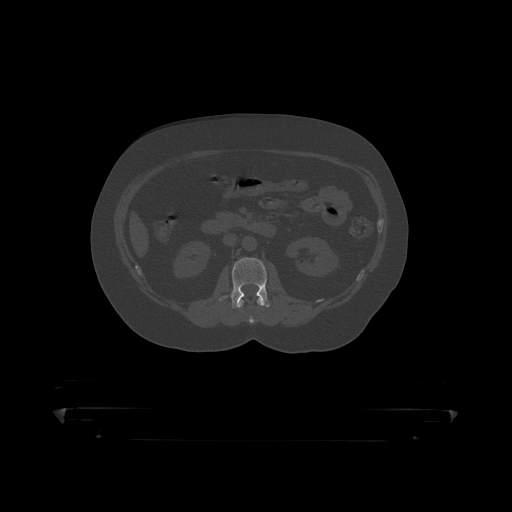
CT including the spine, one axial slice. Position 125 of 390 along the scan axis. 120 kVp. Bone window (W 1800 / L 400 HU). 1.25 mm slice thickness. 512 × 512 image matrix, field of view 650 × 650 mm. Male patient, age 60 years. Case-level facts recorded for this patient, not image findings: primary cancer: prostate.
Outlined on this slice (semi-automatically segmented with operator editing):
- L1 vertebra: bounding box (x1, y1, x2, y2) in pixels: (239, 299, 264, 319)
- L2 vertebra: (219, 258, 270, 309)